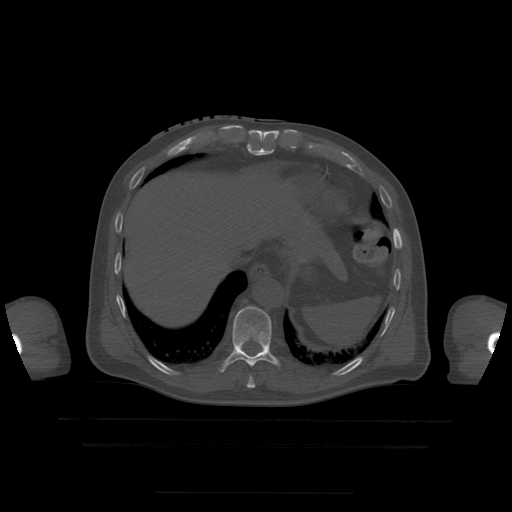
CT including the spine, one axial slice; bone window (W 1800 / L 400 HU); 1.25 mm slice thickness; 512 × 512 image matrix. Patient age 68 years. Case-level facts recorded for this patient, not image findings: primary cancer: urothelial.
Outlined on this slice (semi-automatic segmentation, software-assisted and operator-edited):
- T10 vertebra: bounding box (x1, y1, x2, y2) in pixels: (221, 307, 279, 372)
- T9 vertebra: (247, 377, 255, 389)